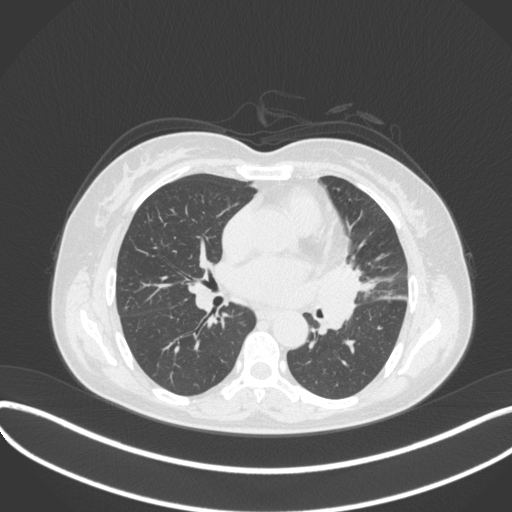
Chest CT, one axial slice. Slice 180 of 373 in the series (ordered by position). Lung window (W 1500 / L -600 HU). 1 mm slice thickness. 512 × 512 image matrix, field of view 400 × 400 mm. Female patient, age 54 years. Case-level facts recorded for this patient, not image findings: clinical TNM (as recorded): T2a N1 M0; histopathological grade: G3.
Structures marked on this image (bounding box drawn by a radiologist):
- lung tumour (recorded histology: small cell carcinoma): bounding box (x1, y1, x2, y2) in pixels: (308, 254, 365, 338)